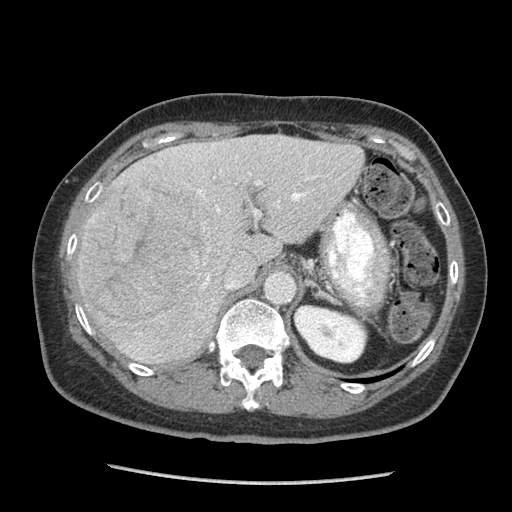
Contrast-enhanced abdominal CT (liver protocol), one axial slice; position 58 of 105 along the scan axis; soft-tissue window (W 400 / L 40 HU); 2.5 mm slice thickness; 512 × 512 image matrix. From the clinical record (not read from this slice): diagnosis: hepatocellular carcinoma (patient treated with transarterial chemoembolisation; whether this scan precedes or follows treatment is not stated here); TNM stage (as recorded): Stage-I; Child-Pugh class: A; tumour differentiation: moderately differentiated; tumour nodularity: uninodular.
Annotated regions visible in this slice (semi-automatically segmented with operator editing):
- liver parenchyma outside the tumour (the mass and vessels are separate outlines, so this box may not span the whole liver): bounding box [x1, y1, x2, y2] px = [75, 134, 364, 364]
- mass: [79, 182, 216, 334]
- liver vessels: [138, 144, 316, 360]